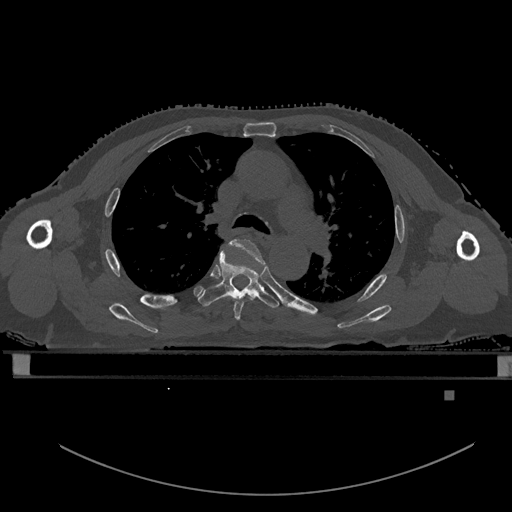
CT including the spine, one axial slice. Slice 375 of 969 in the series (ordered by position). Bone window (W 1800 / L 400 HU). 512 × 512 image matrix, field of view 456 × 456 mm. Male patient, age 82 years. From the clinical record (not read from this slice): primary cancer: prostate; vertebrae with lytic lesions (as recorded): T11, T9, T8, T2.
Outlined on this slice (semi-automatically segmented with operator editing):
- T4 vertebra: bounding box [x1, y1, x2, y2] px = [230, 238, 265, 320]
- T5 vertebra: [198, 250, 279, 308]